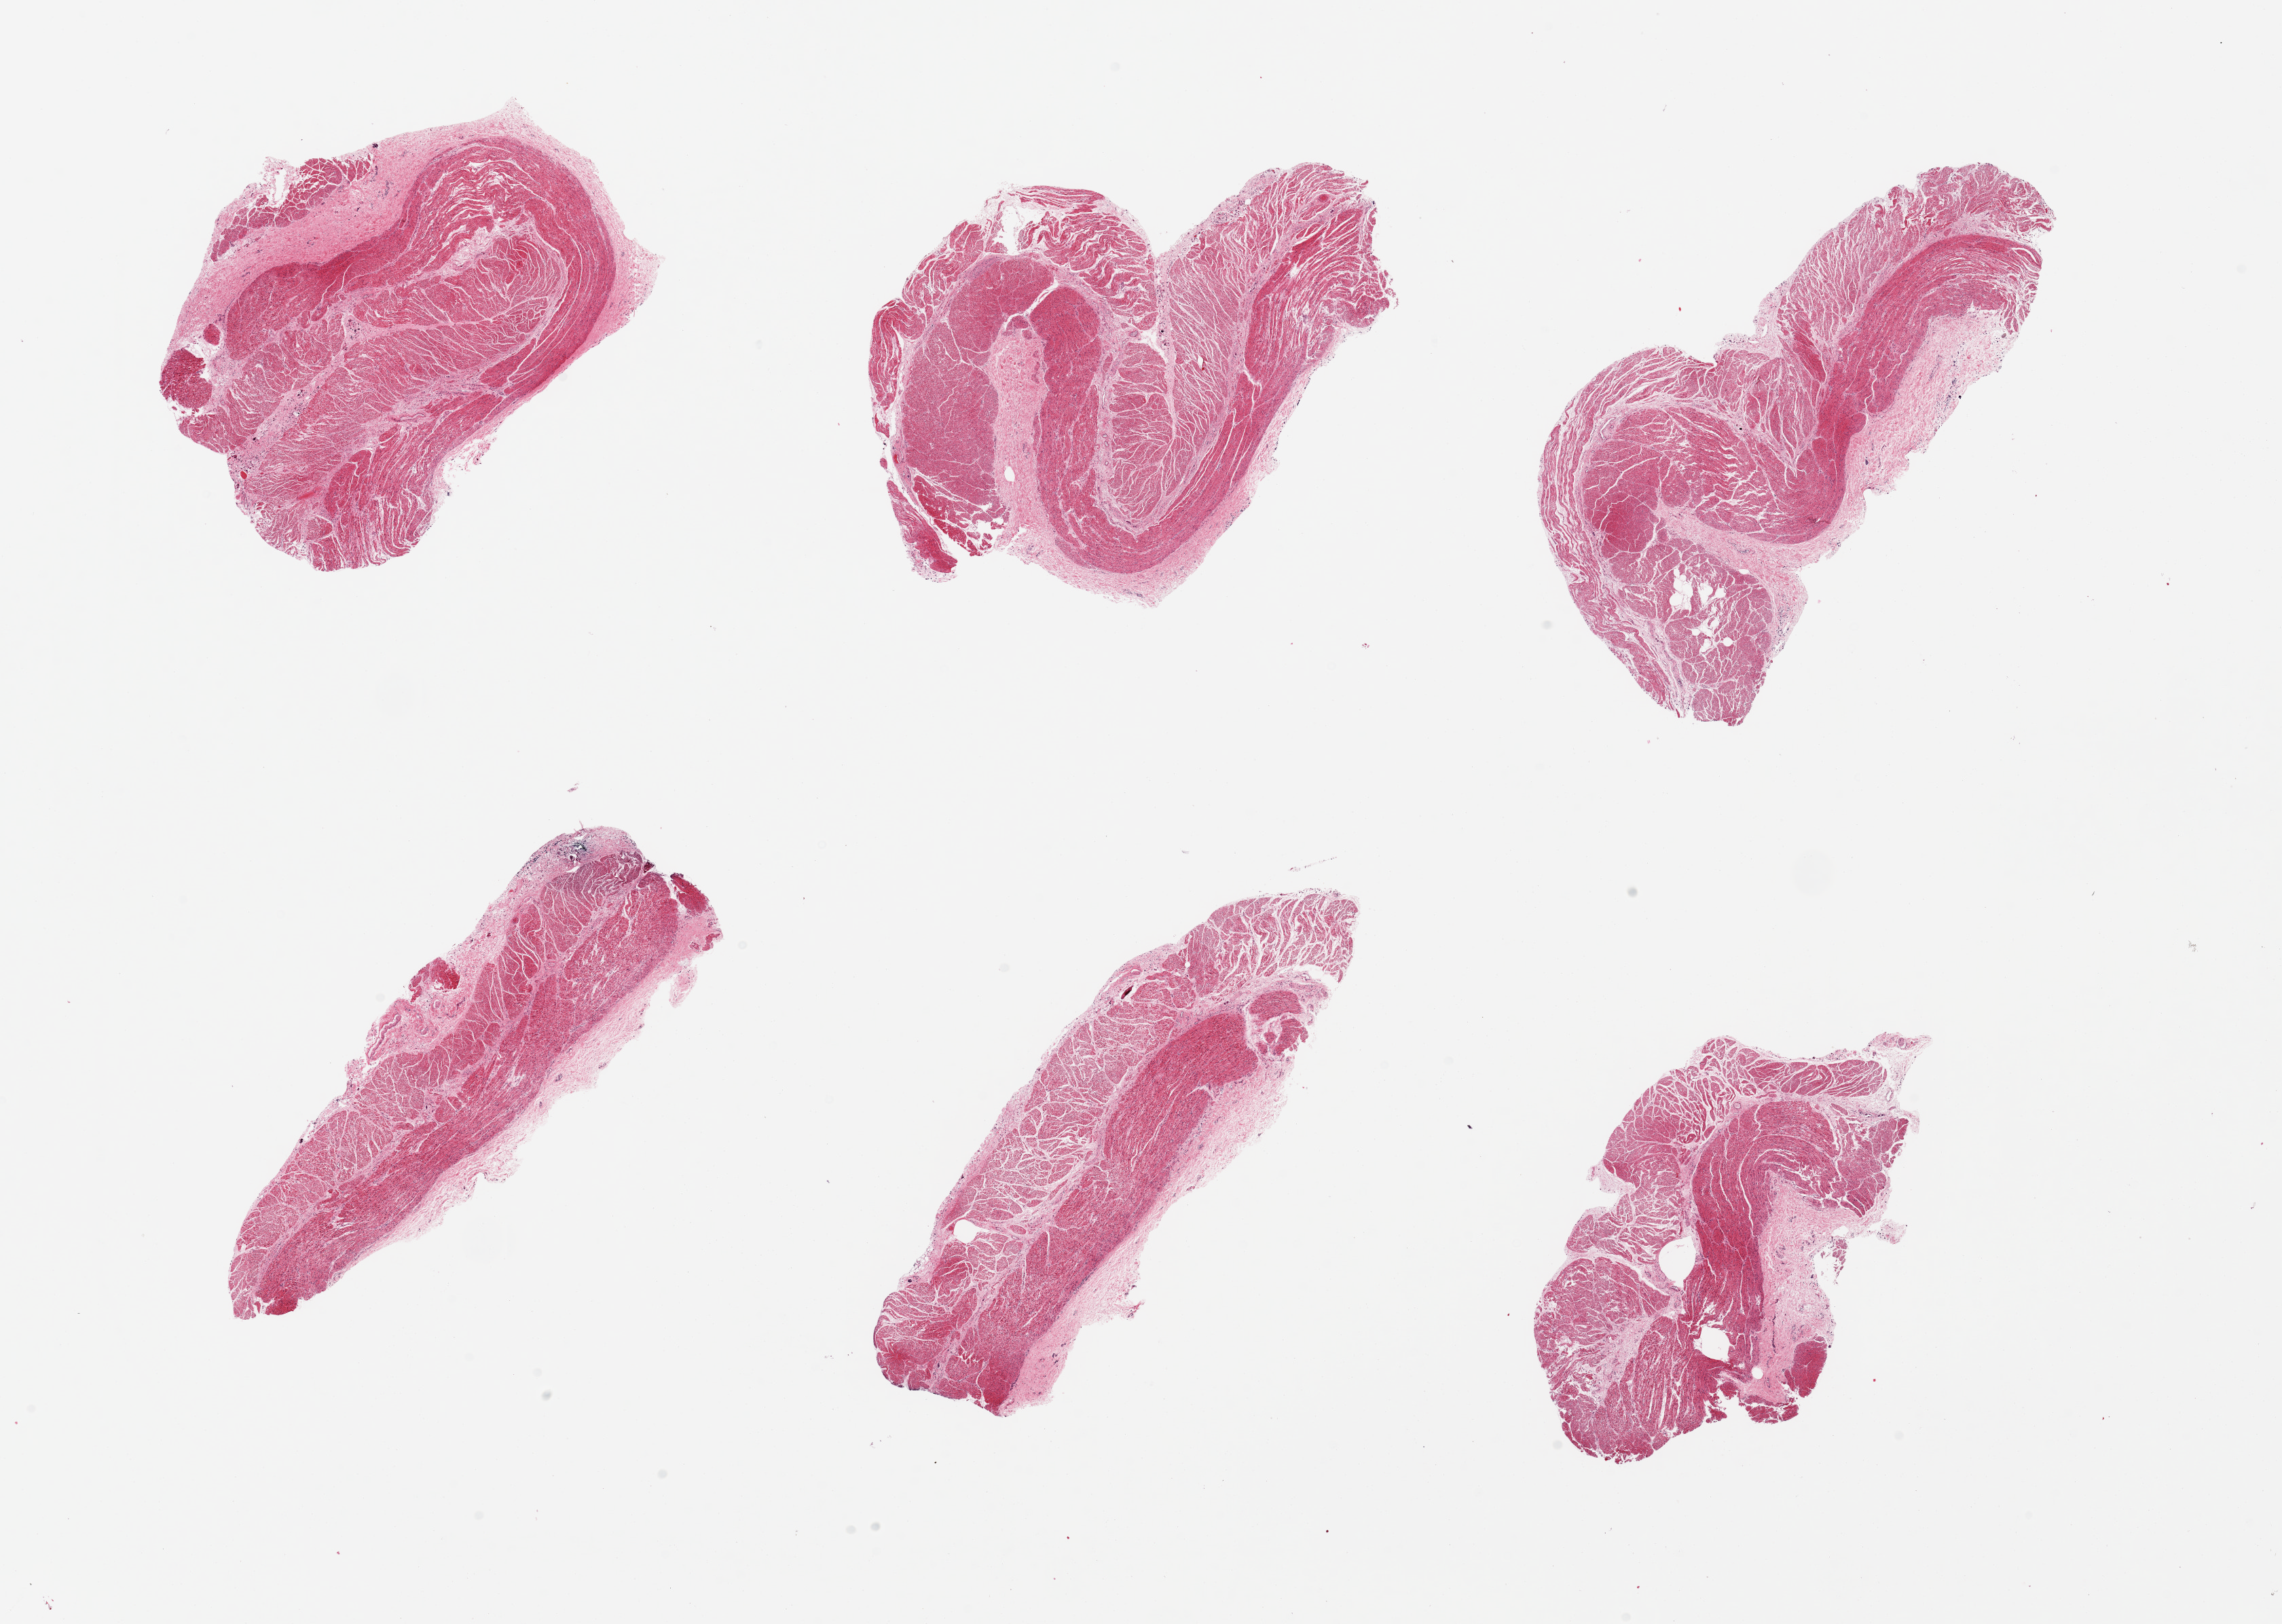
Whole-slide image, hematoxylin and eosin (H&E) stain — whole scanned area (about 26.6 x 18.9 mm) shown as a low-resolution overview; PAXgene-fixed paraffin-embedded (PFPE) section; section of esophageal mucous membrane (target tissue); tissue donor sample. Donor sex: male.
Reviewer comment on this tissue sample: 6 pieces, all muscularis/connective tissue, no mucosa visible, completely sloughed.